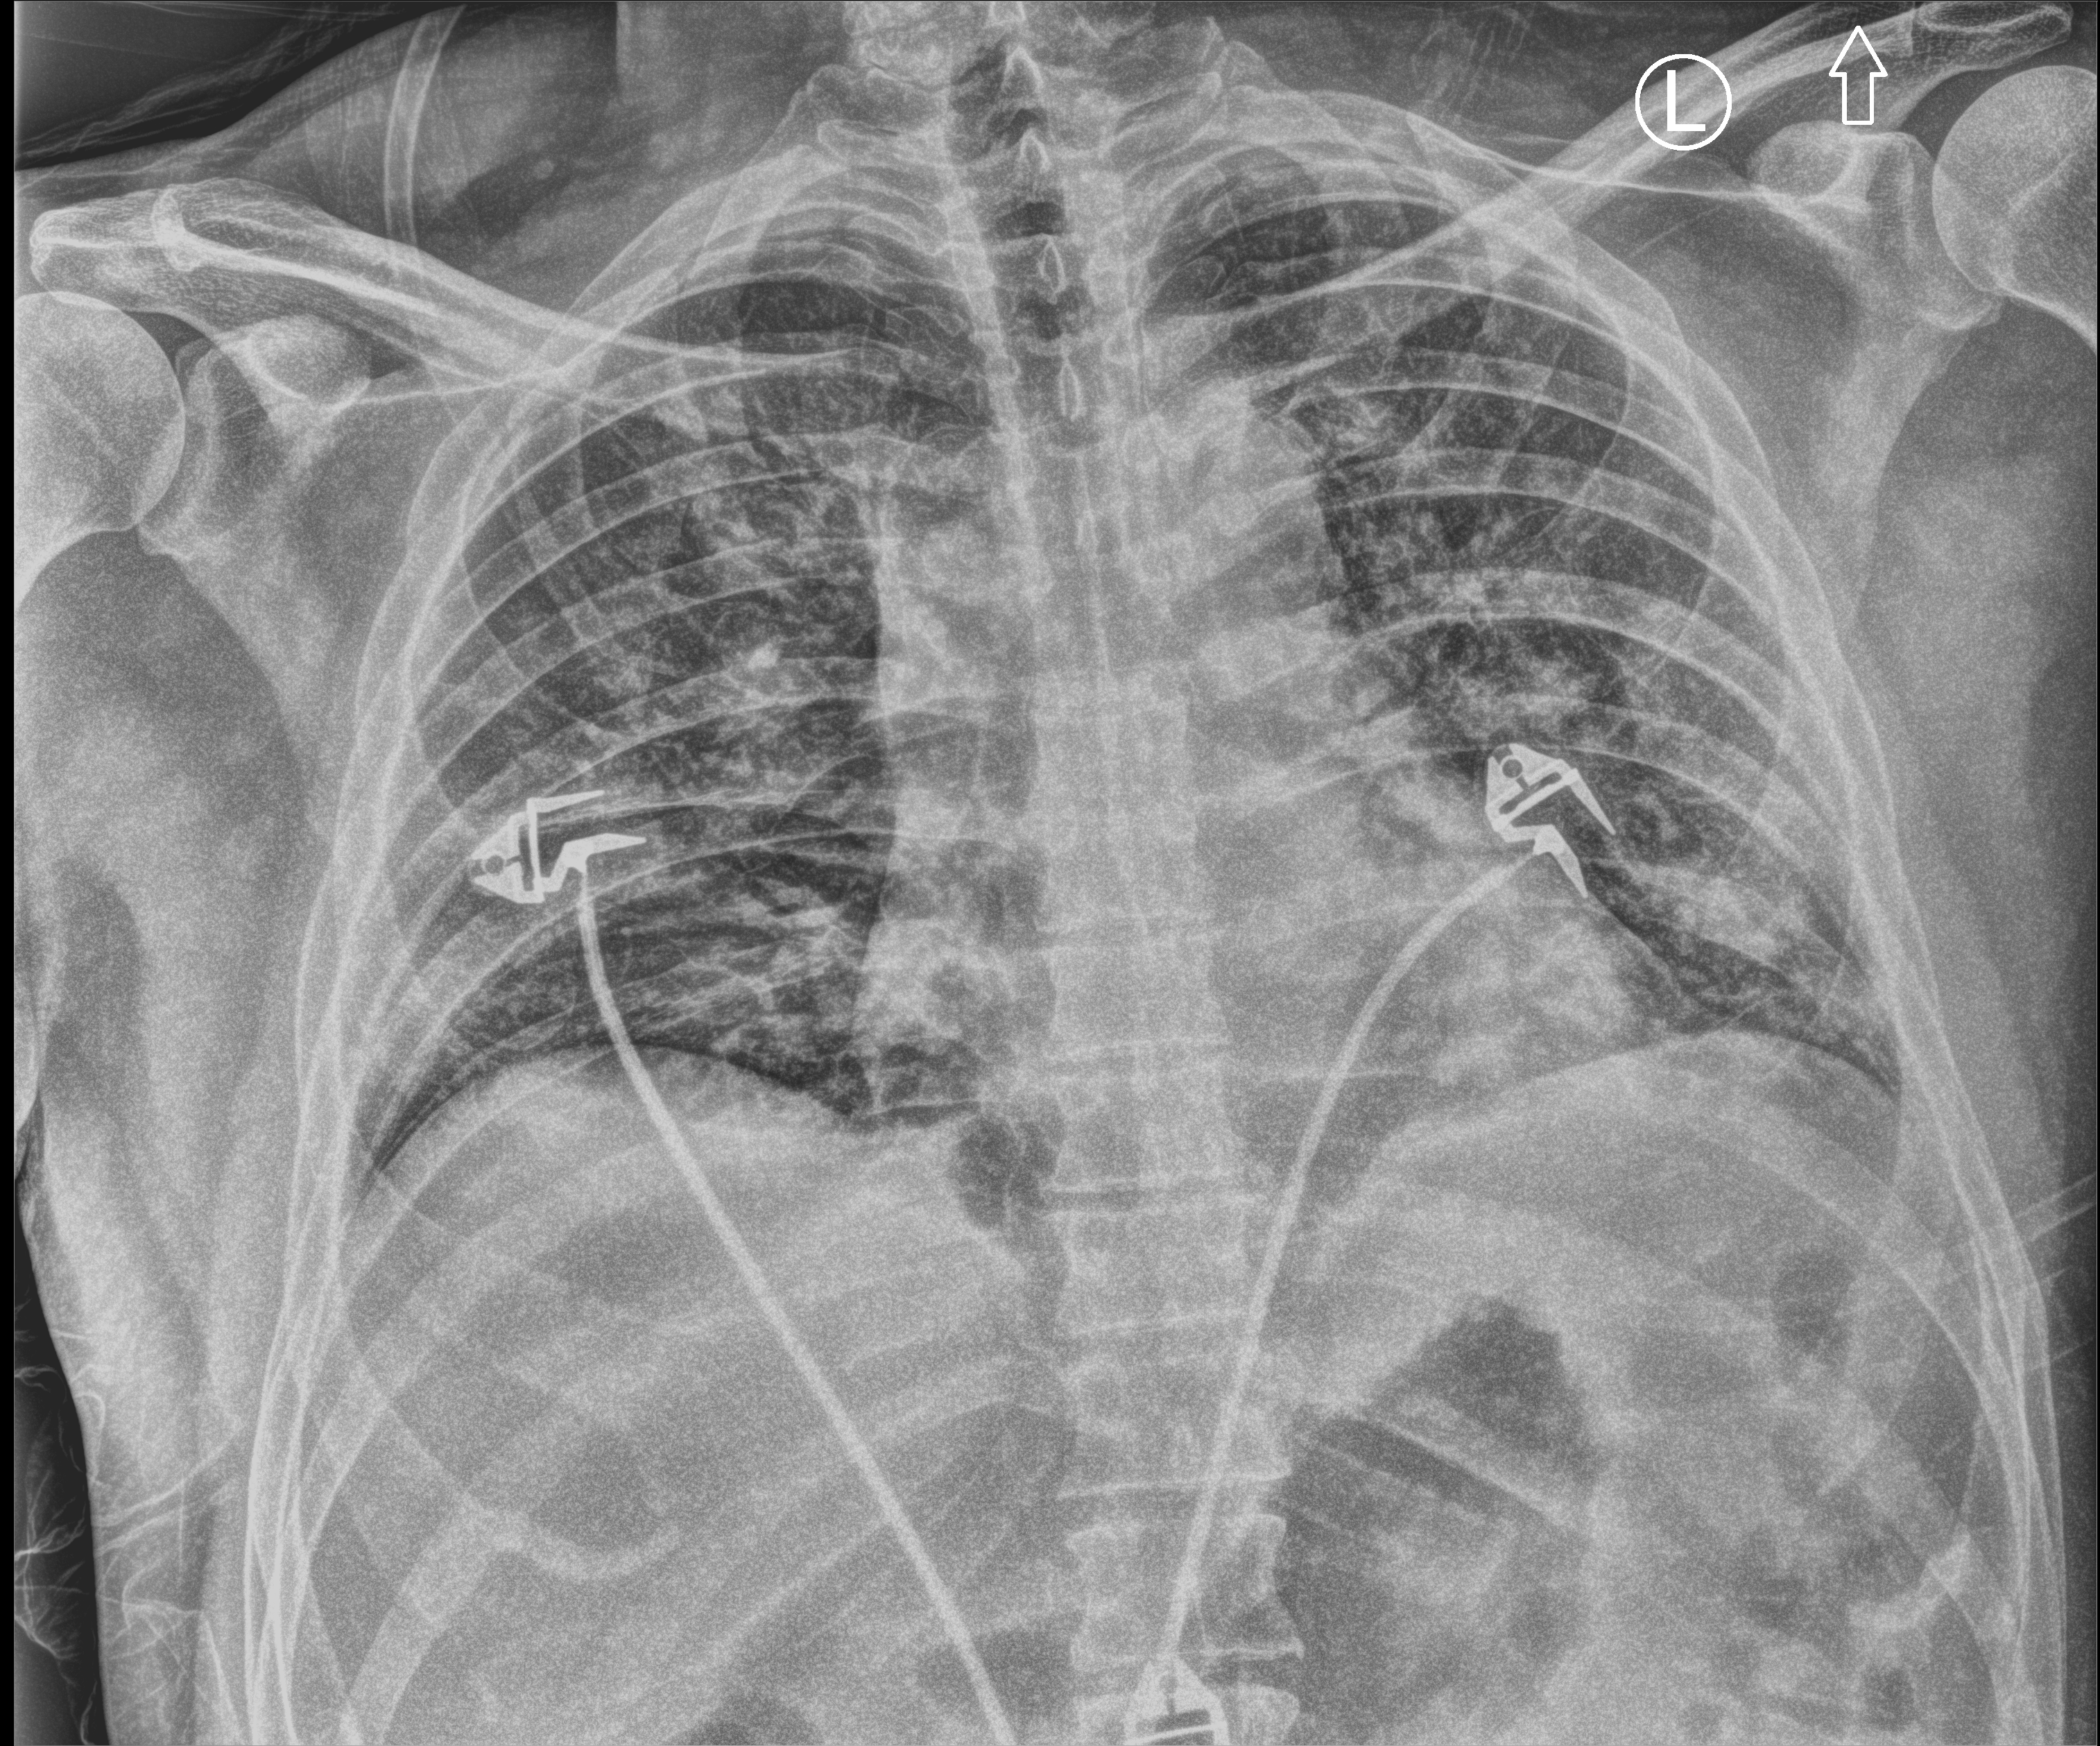
Chest X-ray (portable), anteroposterior (AP) projection. Patient hospitalised with COVID-19; male, aged 18–59 years.
Hospital-stay facts (about this admission, not read from this image; timing relative to this image not recorded):
- other chronic lung disease (admission record): no
- admitted to intensive care during this hospital stay: yes